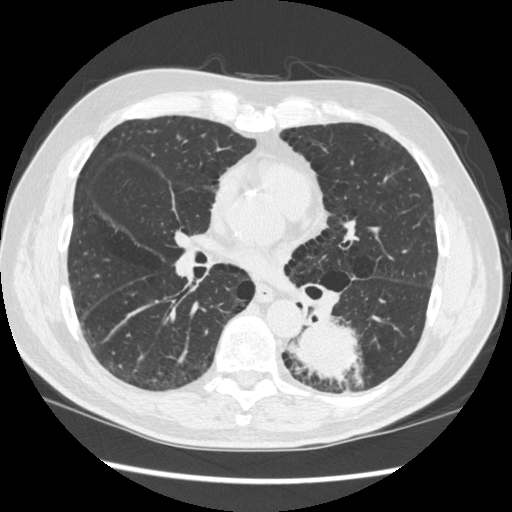
Low-dose screening chest CT, axial slice; baseline annual screen; lung window (W 1500 / L -600 HU); 120 kVp; slice 161 of 348 in the series. Male participant, aged 72 years at enrolment.
Expert reader's lesion annotation, bounding box <265,305,369,398> (left, top, right, bottom; pixels). The screening reader recorded 2 non-calcified nodules or masses ≥4 mm on this exam (left lower lobe, right middle lobe); which of them this box marks is not recorded. Lung cancer was diagnosed 37 days after this screen: squamous cell carcinoma, NOS, left lower lobe, stage IIIA (AJCC 6th edition), 60 mm at pathology.